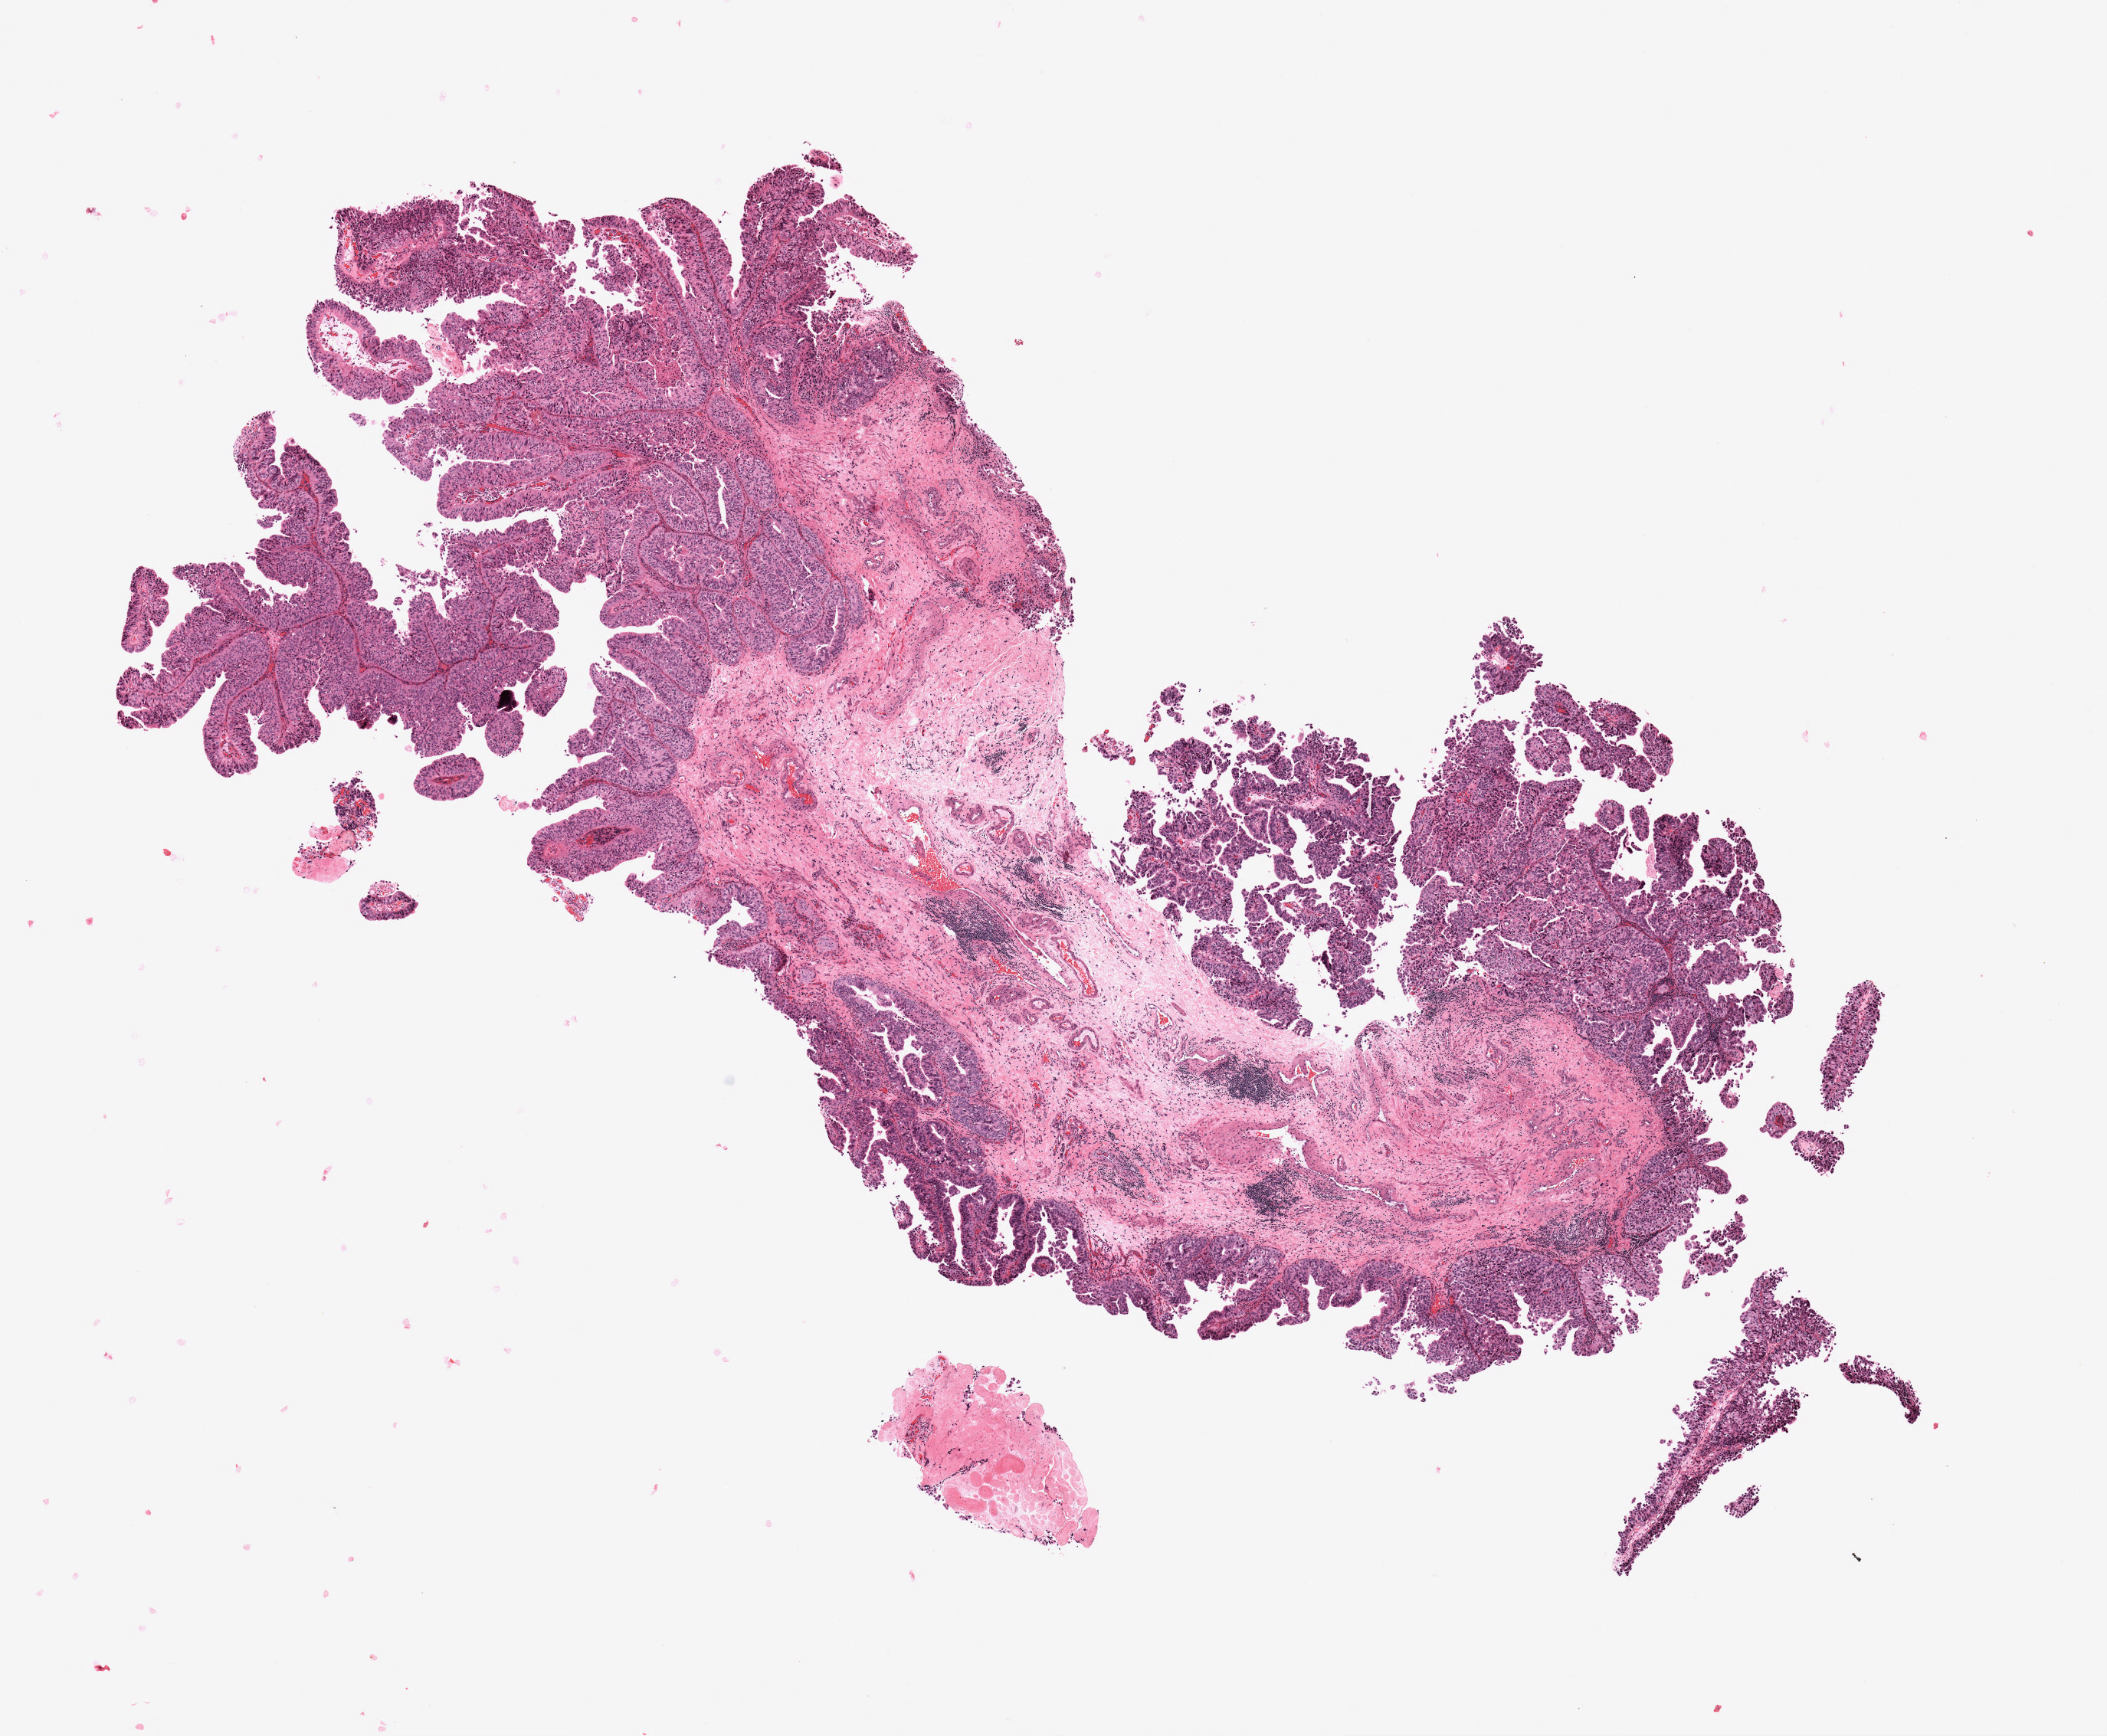
Whole-slide histology image, H&E-stained, shown as a low-resolution overview of the whole scanned area (about 11.0 x 9.0 mm, slide scanned at 20x); formalin-fixed paraffin-embedded (FFPE) diagnostic section; primary tumour sample from the bladder. Patient: male, age at initial diagnosis 75 years. Histologic grade: high grade.
- lymph nodes positive (case pathology): 0 of 46 examined
- pathologic diagnosis: Papillary transitional cell carcinoma
- AJCC pathologic stage: III (7th edition)